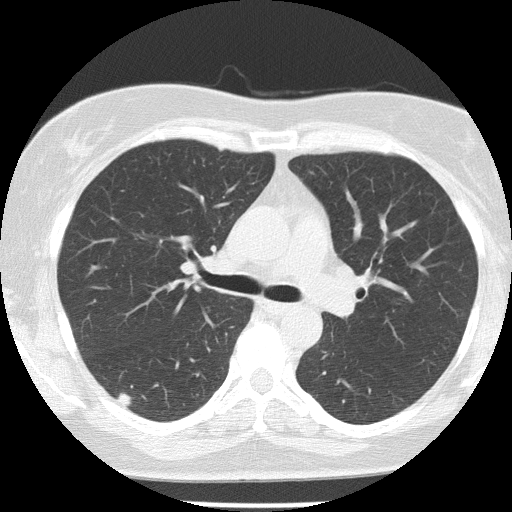
Low-dose screening chest CT, axial slice; baseline annual screen; lung window (W 1500 / L -600 HU); lung (sharp) reconstruction kernel (FC51); 120 kVp; slice 58 of 142 in the series; 512 × 512 image matrix. Female, age 58 years at enrolment. Former smoker at enrolment.
- Expert-annotated lung lesion, bounding box (x1, y1, x2, y2) in pixels: (99, 374, 151, 423).
- The screening reader recorded 2 non-calcified nodules or masses ≥4 mm on this exam; which of them this box marks is not recorded.
- Official screen result: positive, change unspecified: nodule(s) >= 4 mm or enlarging nodule(s), mass(es), or other non-specific abnormalities suspicious for lung cancer.
- Later outcome: lung cancer diagnosed 648 days after this screen (after the second annual screen) — adenocarcinoma, NOS, right lower lobe, well differentiated (G1), stage IB (AJCC 6th edition), 10 mm at pathology.